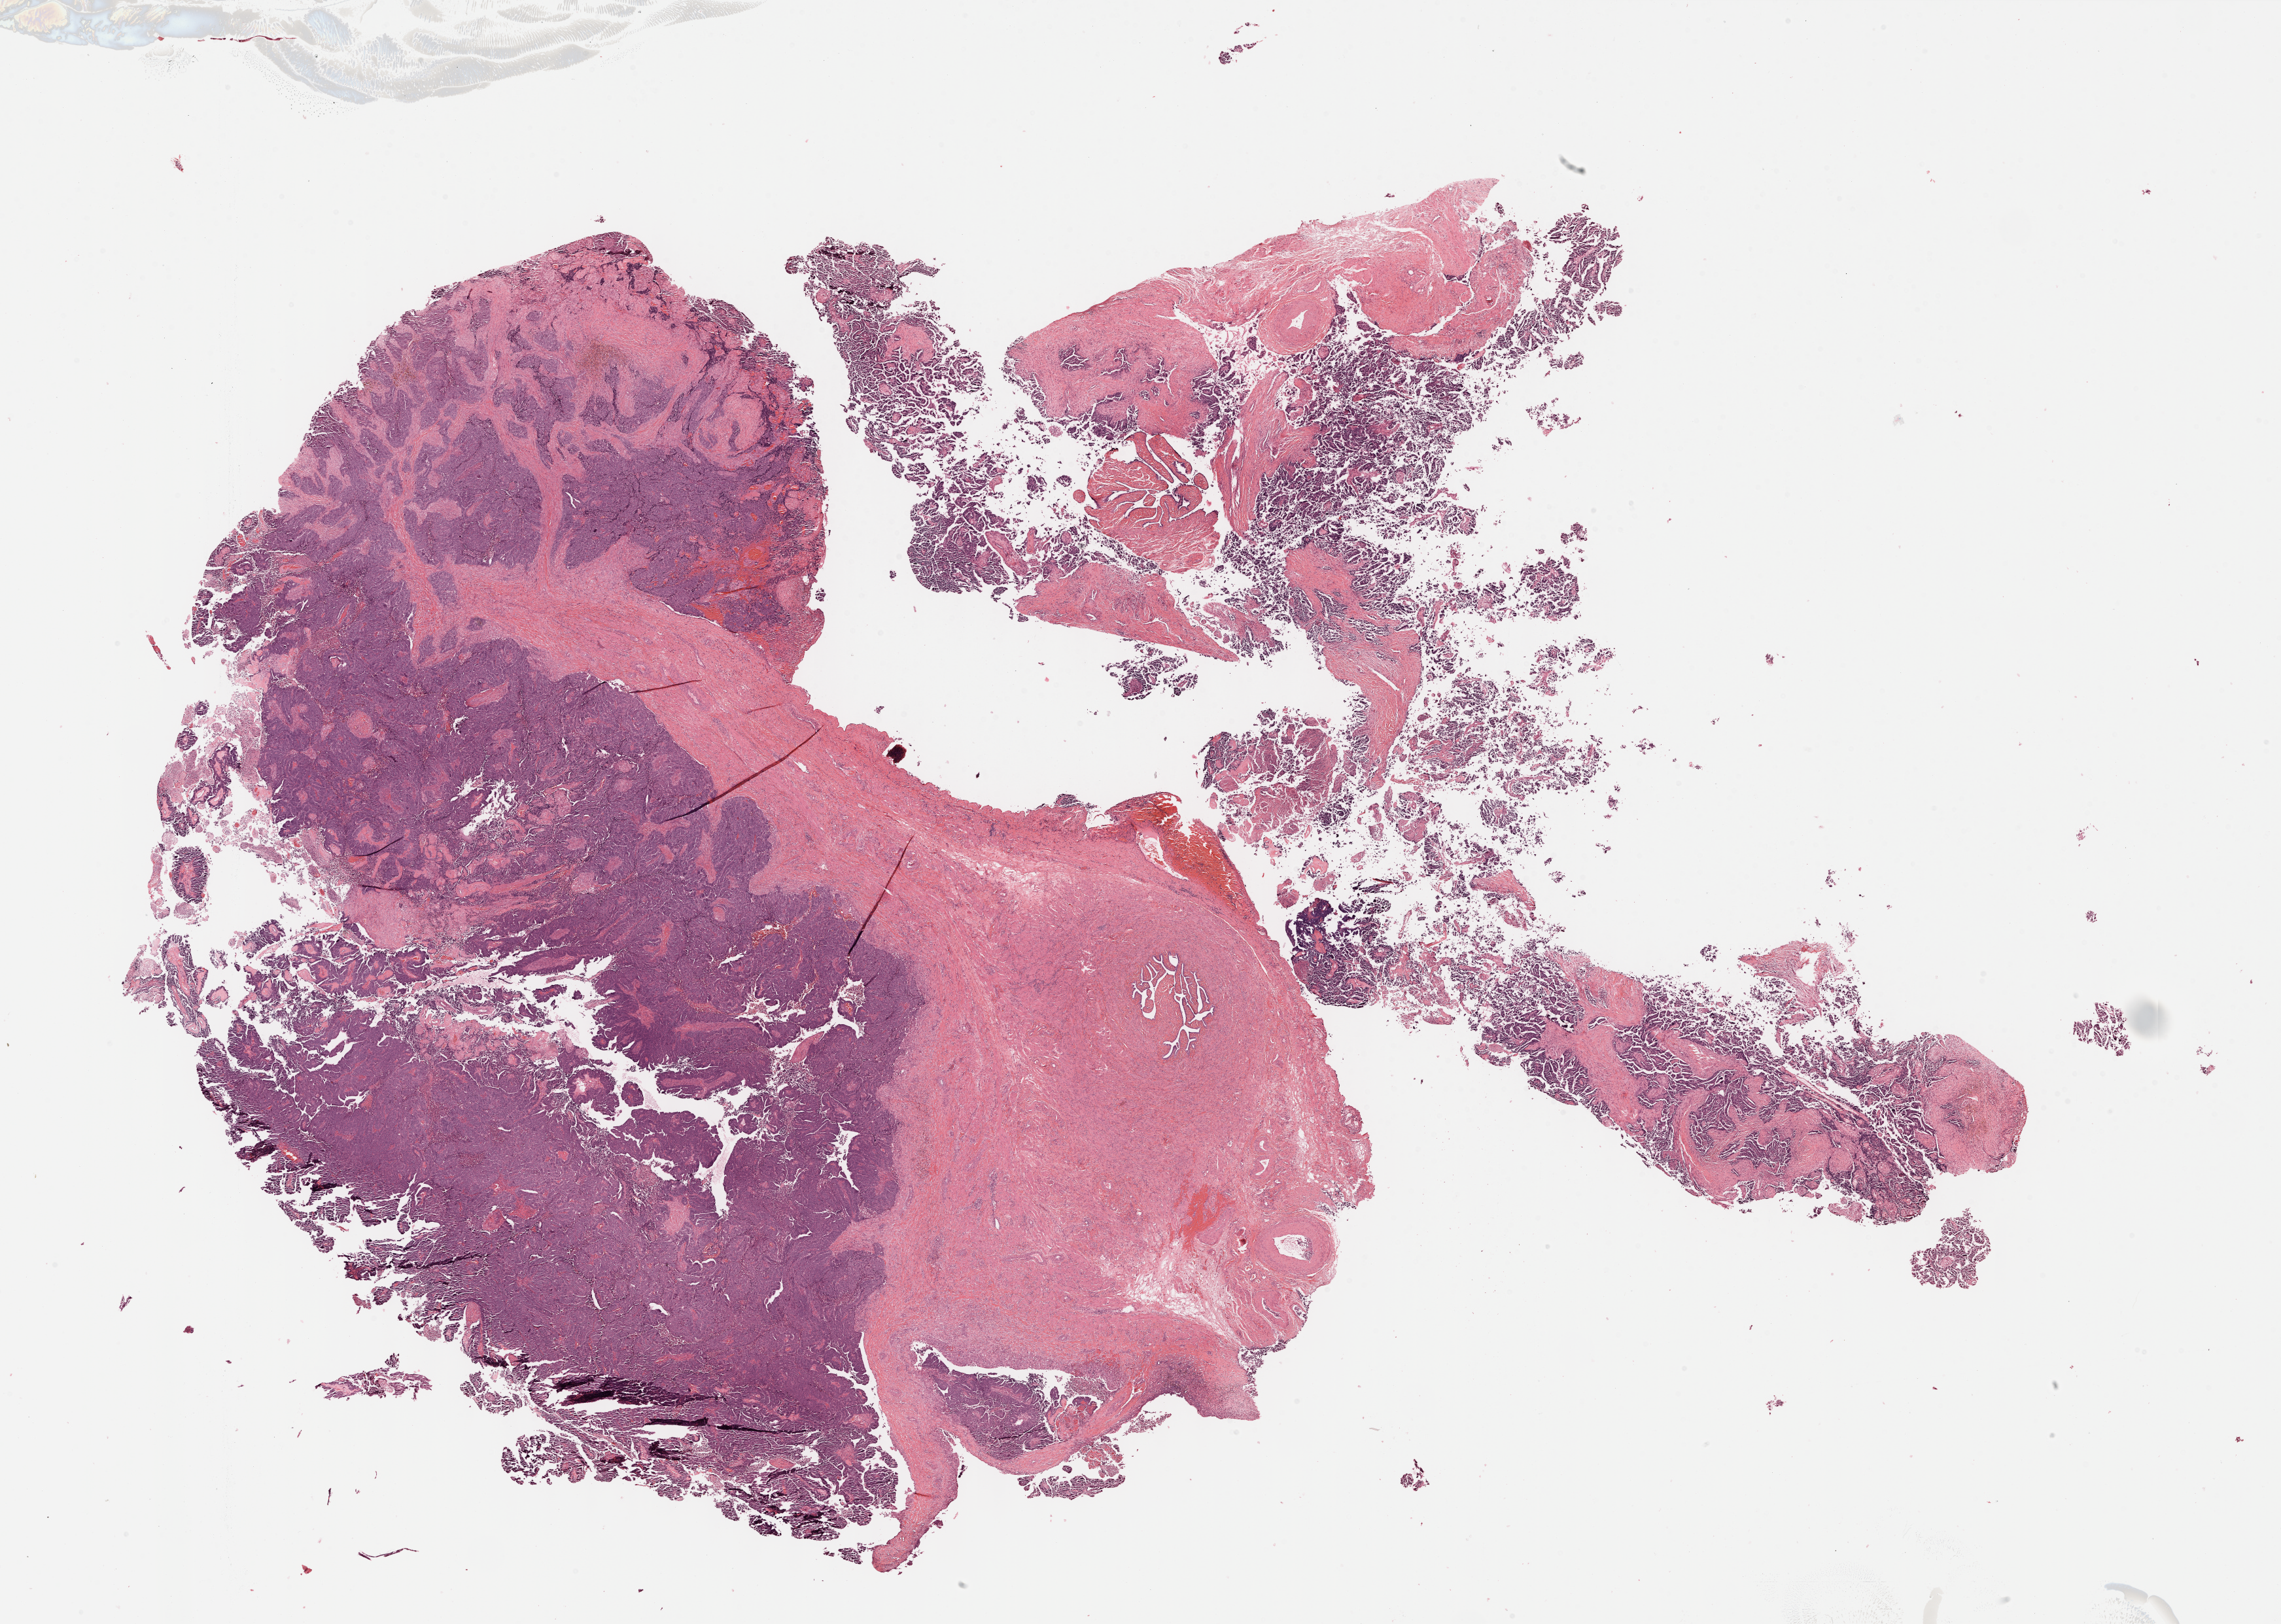
Whole-slide histology image, H&E — whole scanned area (about 28.2 x 20.1 mm, acquisition: 40x scan) shown as a low-resolution overview, formalin-fixed paraffin-embedded (FFPE) diagnostic section, ovary, primary tumour sample. Female, age 80 years at initial diagnosis. Histologic grade: G3 (poorly differentiated).
* FIGO stage: IIIC
* diagnosis: Serous cystadenocarcinoma, NOS